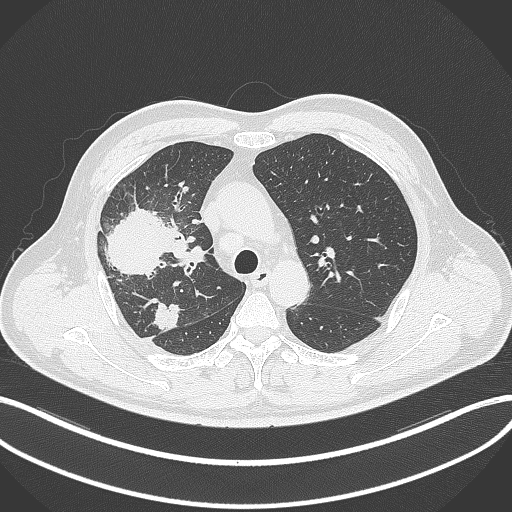
Chest CT, one axial slice. Position 232 of 348 along the scan axis. Reconstruction kernel B70f. 120 kVp. Lung window (W 1500 / L -600 HU). 1 mm slice thickness. 512 × 512 image matrix, field of view 400 × 400 mm. Patient: male, 55 years. From the clinical record (not read from this slice): clinical TNM (as recorded): T3 N2 M1.
Annotated regions visible in this slice (bounding box drawn by a radiologist):
- lung tumour (recorded histology: adenocarcinoma): bounding box [x1, y1, x2, y2] px = [101, 204, 174, 280]